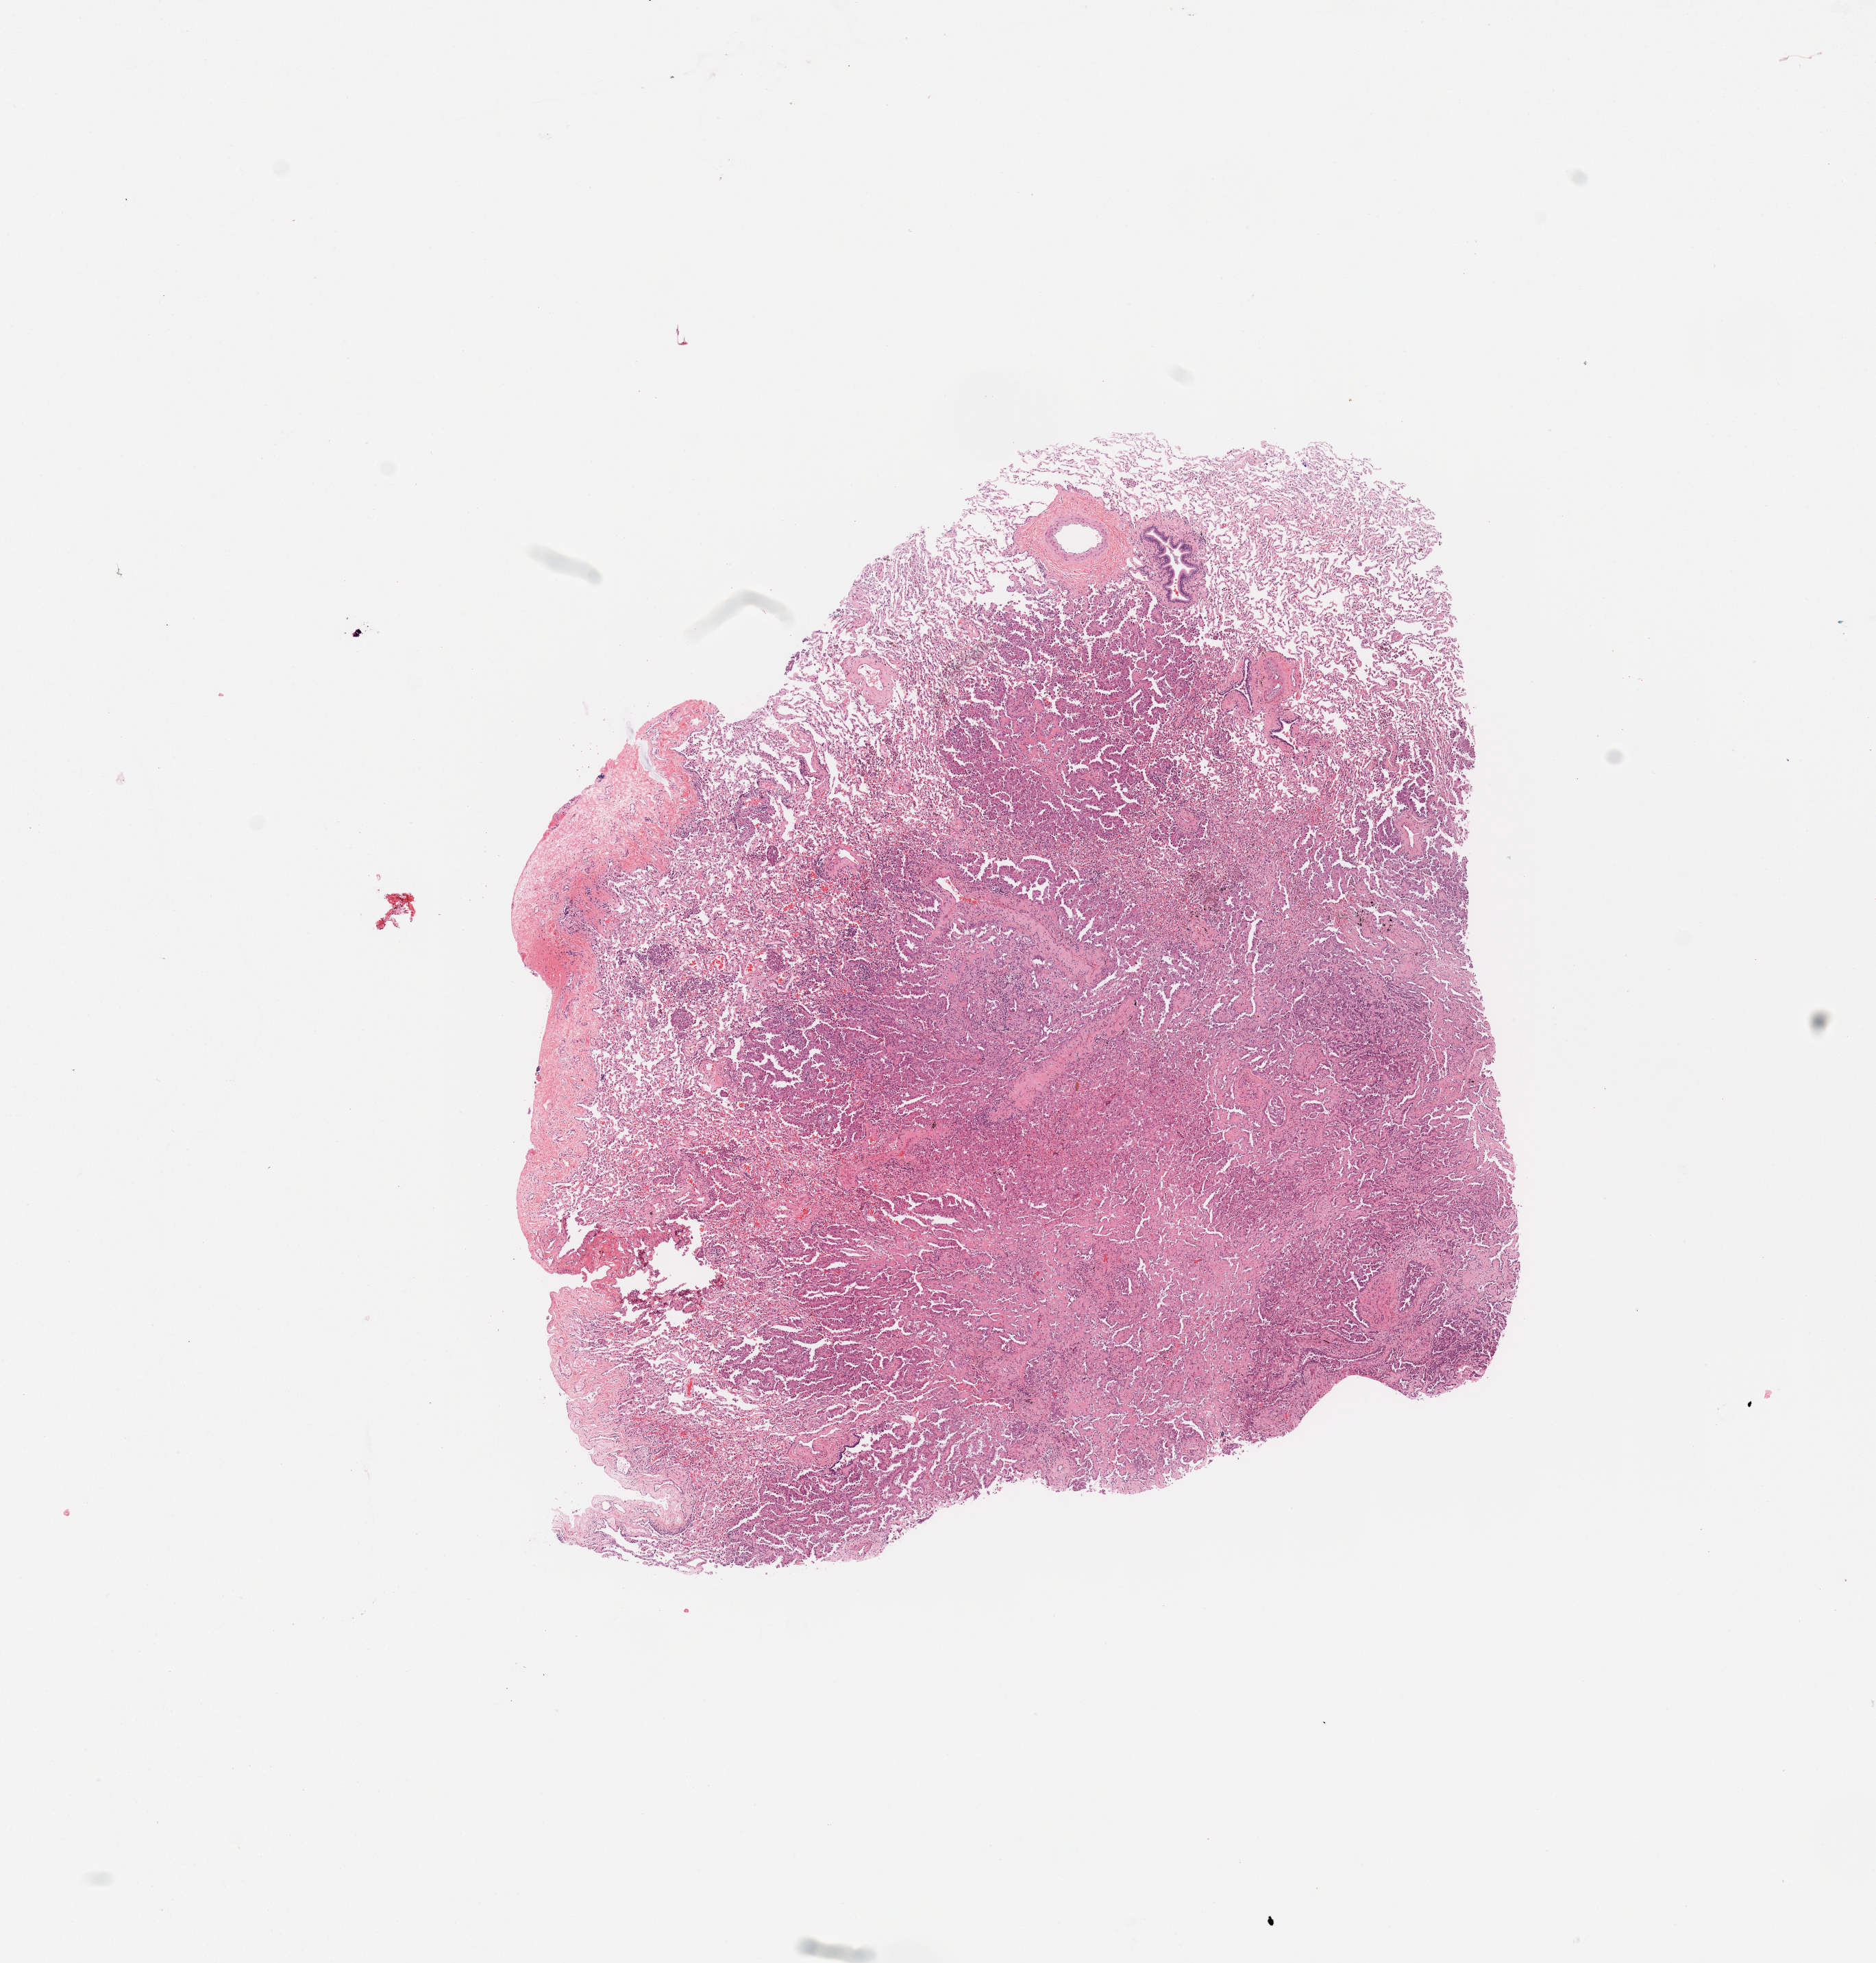
H&E-stained whole-slide image — shown as a low-resolution overview of the whole scanned area (about 10.8 x 11.3 mm), tumour tissue sample, sampled site: lung. Male, 58 y/o. Histologic grade: G3 (poorly differentiated). Pathologist review of this section (percent, as recorded): tumour nuclei 60%, necrosis 2%.
Diagnosis: Adenocarcinoma, NOS. Primary tumour site (as recorded): right lower lobe. AJCC pathologic stage: IA.